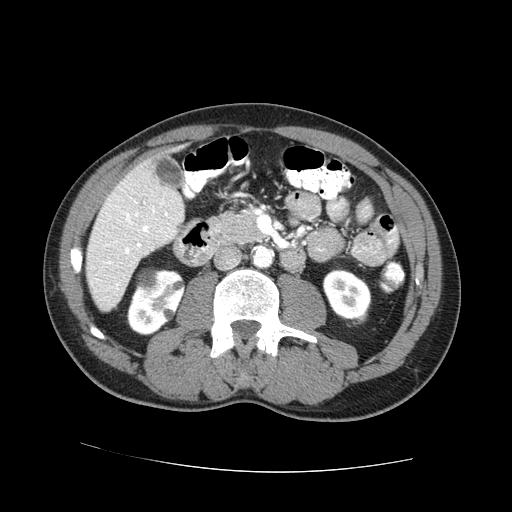
Contrast-enhanced abdominal CT (liver protocol), one axial slice; slice 20 of 73 in the series (ordered by position); one of 2 acquisitions stored at this slice position; soft-tissue window (W 400 / L 40 HU); 512 × 512 image matrix, field of view 380 × 380 mm. Case-level facts recorded for this patient, not image findings: diagnosis: hepatocellular carcinoma (patient treated with transarterial chemoembolisation; whether this scan precedes or follows treatment is not stated here); TNM stage (as recorded): Stage-IVA.
Structures marked on this image (semi-automatic segmentation, software-assisted and operator-edited):
- liver parenchyma outside the tumour (the mass and vessels are separate outlines, so this box may not span the whole liver): bounding box <86,144,184,312> (left, top, right, bottom; pixels)
- liver vessels: <108,209,167,285>